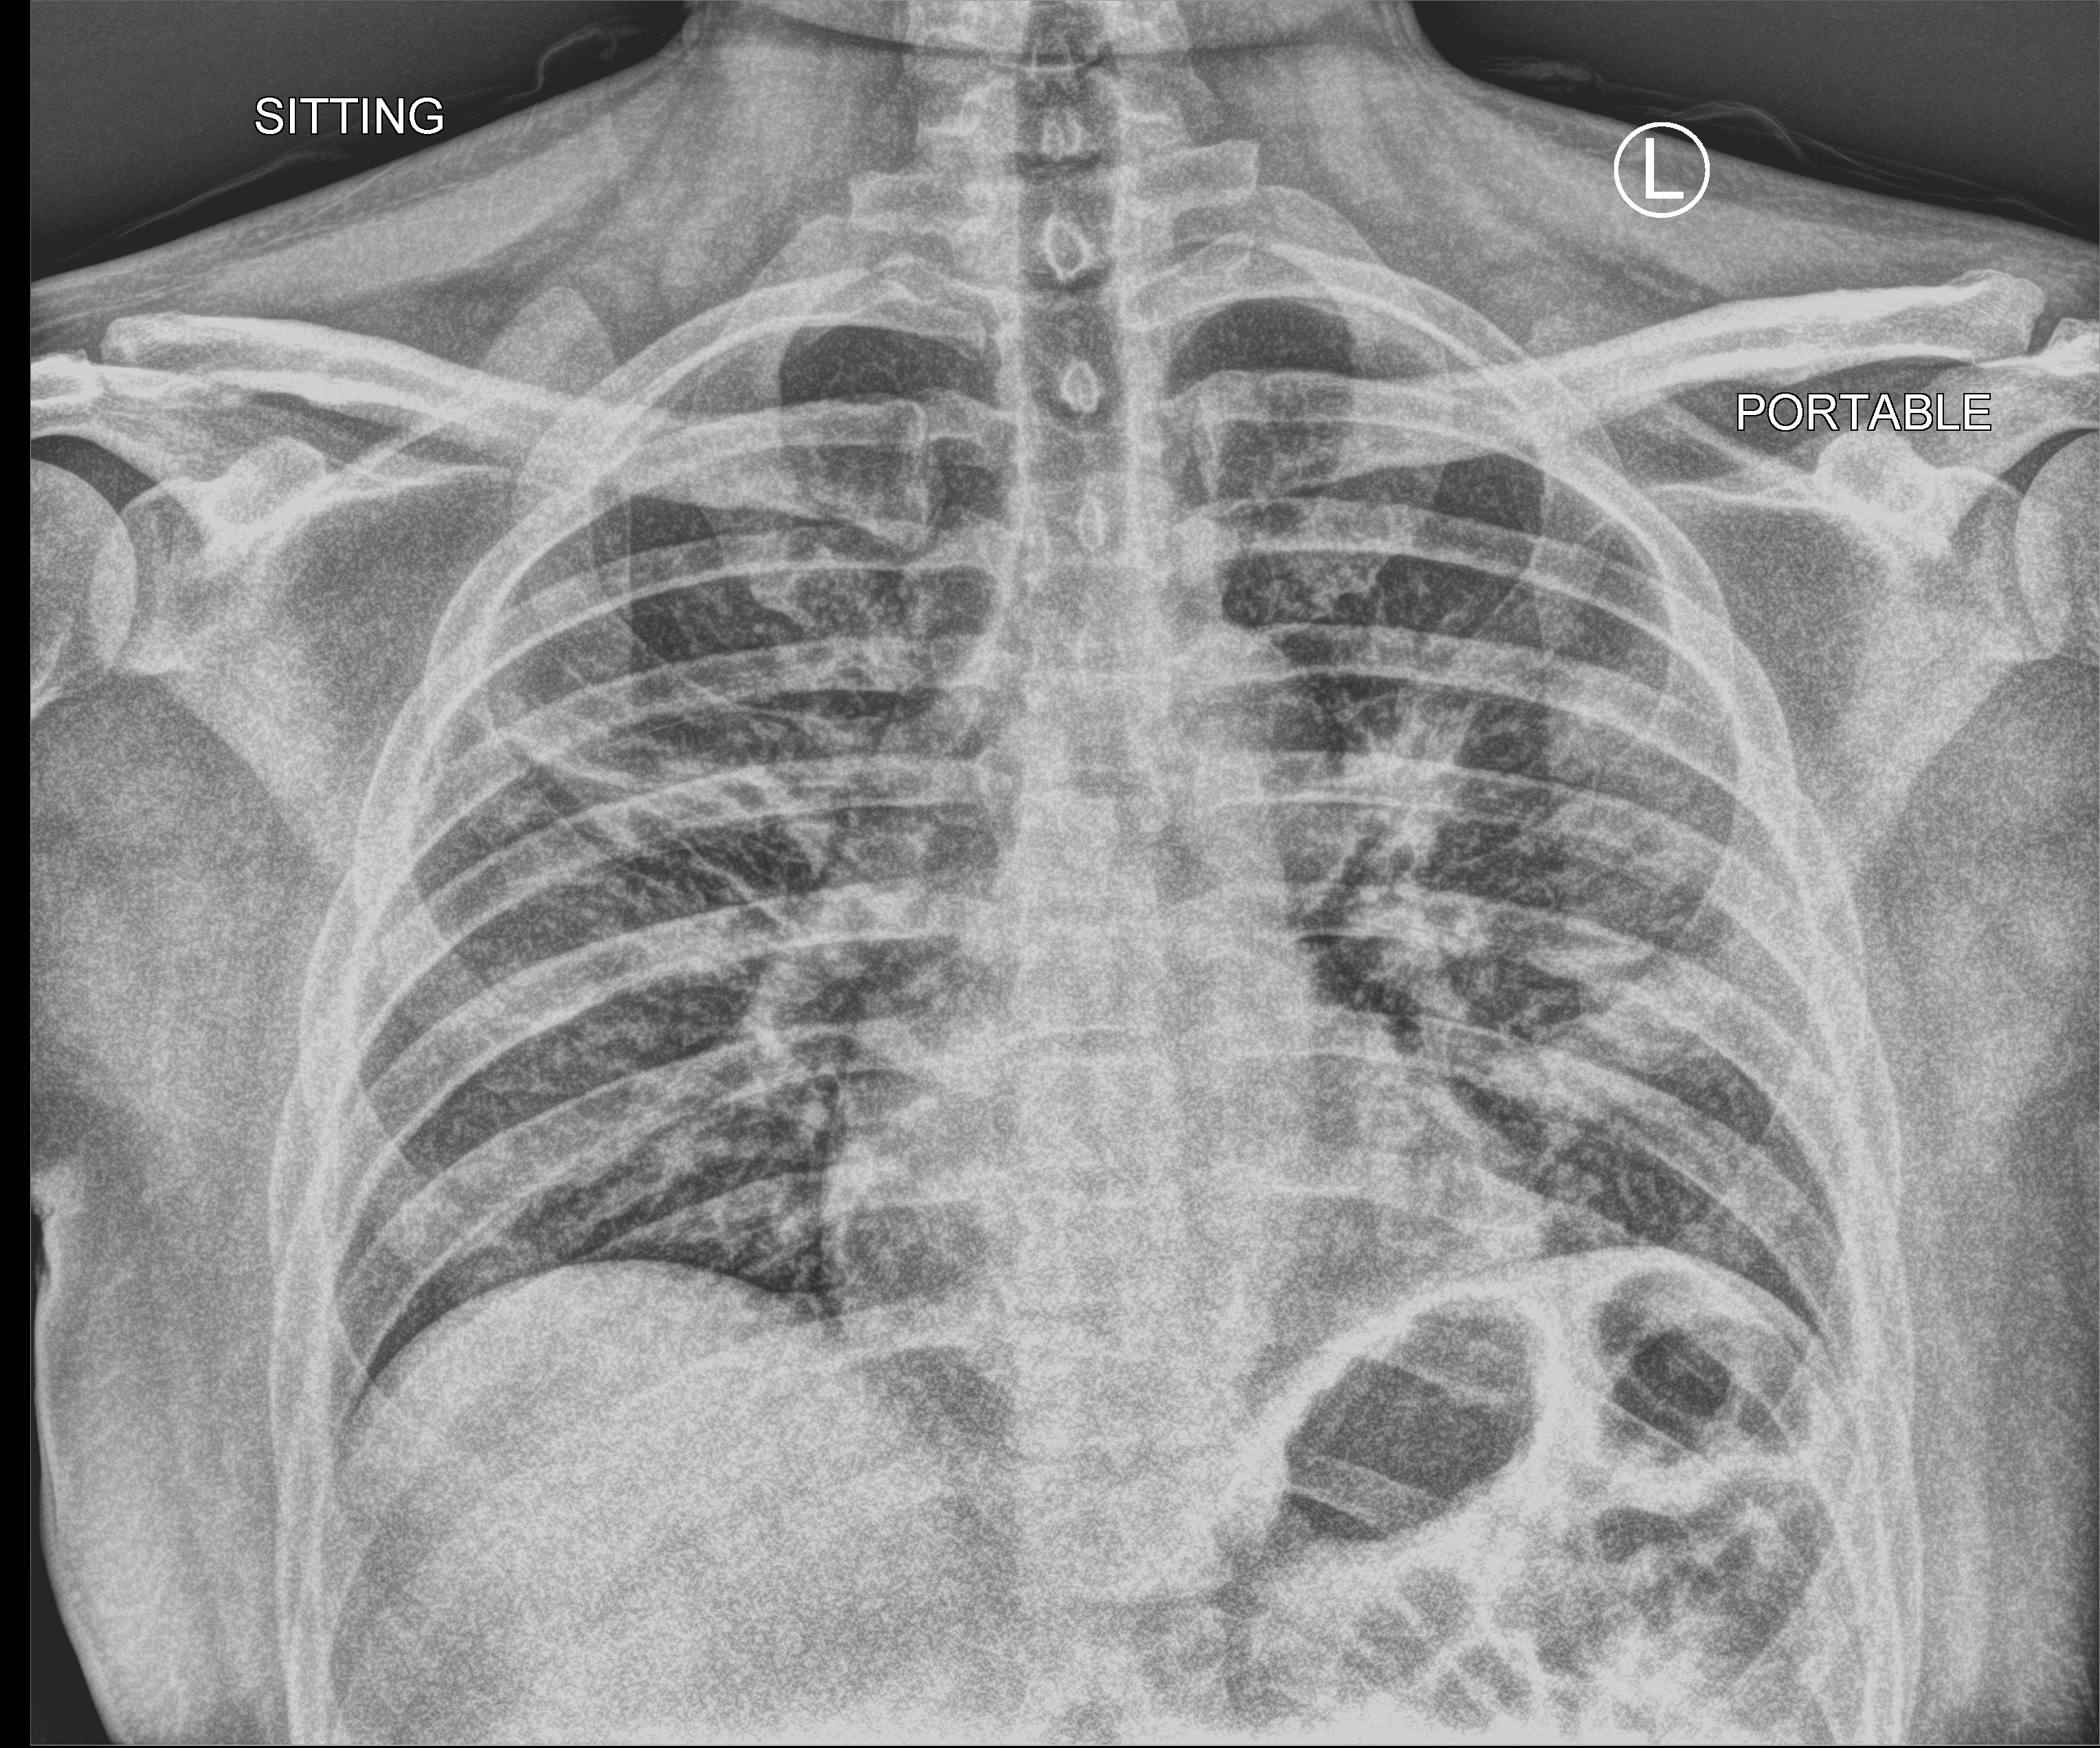
Portable chest radiograph, anteroposterior (AP) projection. Male patient hospitalised with COVID-19, age 18–59 years.
Hospital-stay facts (about this admission, not read from this image; timing relative to this image not recorded): mechanically ventilated during this hospital stay: no.